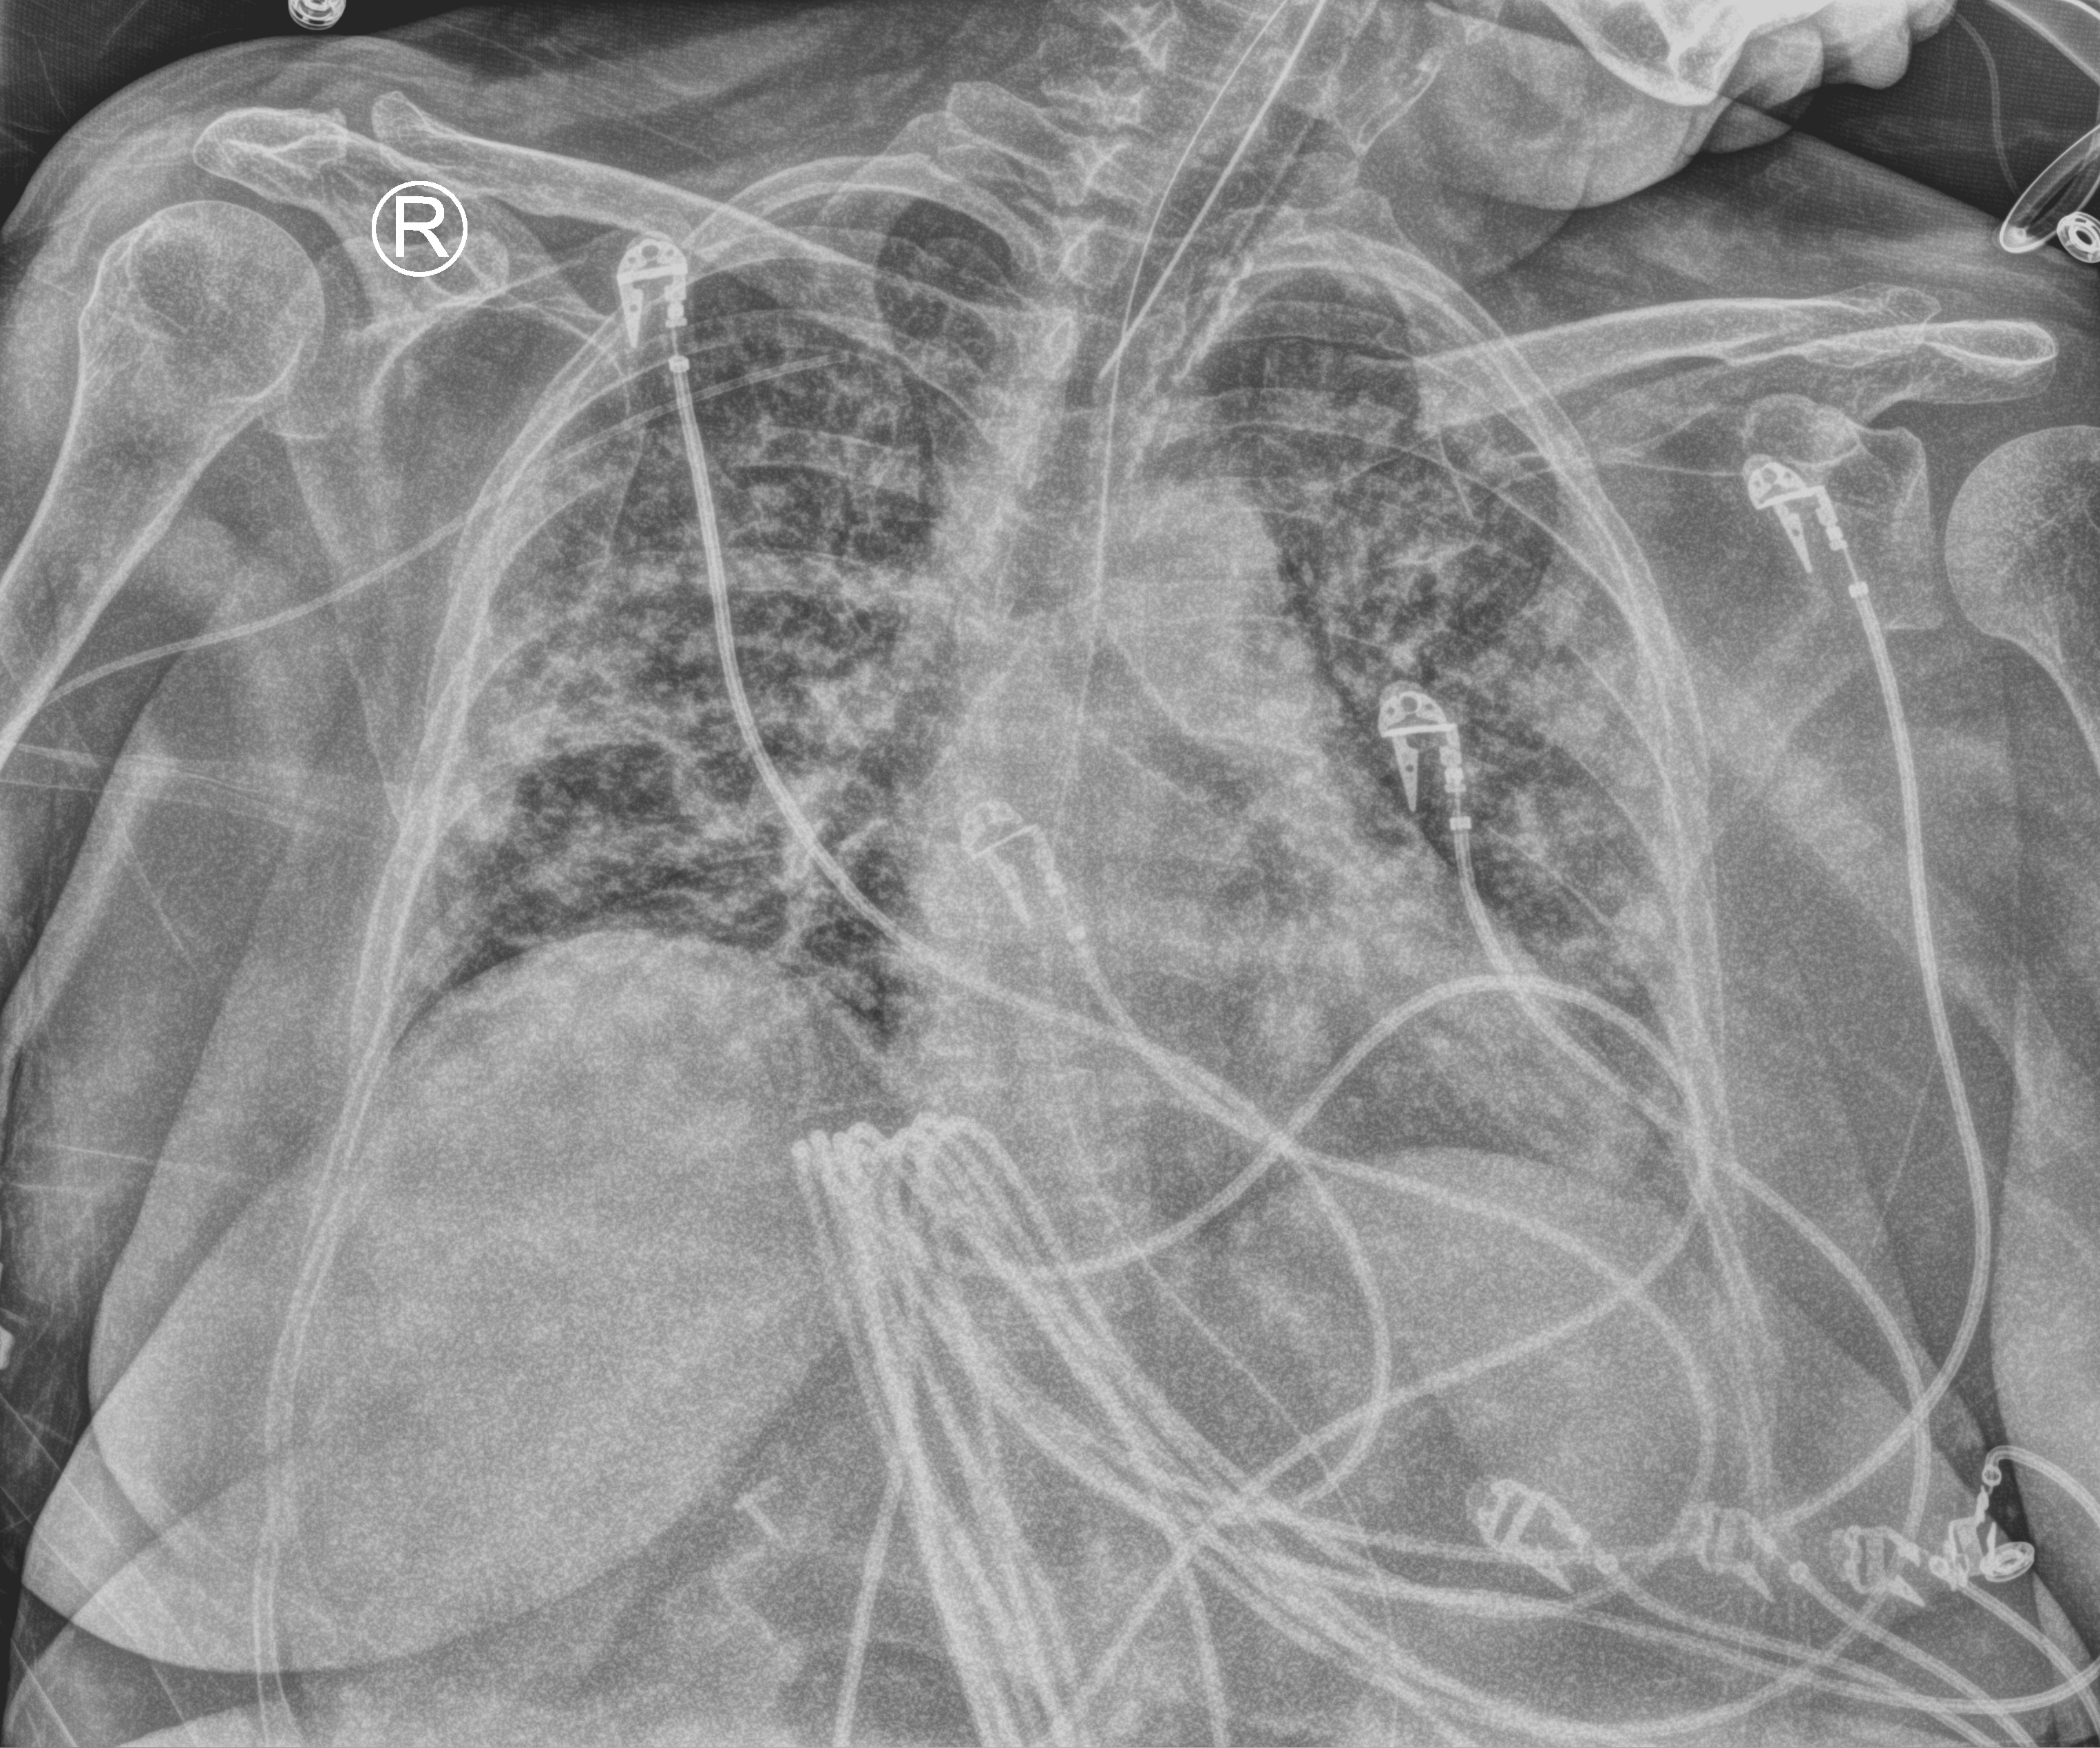
Chest X-ray (portable). Female patient hospitalised with COVID-19, age 18–59 years.
Admission-level facts for this patient (not findings on this image; timing relative to this image not recorded): smoking status (admission record): never.